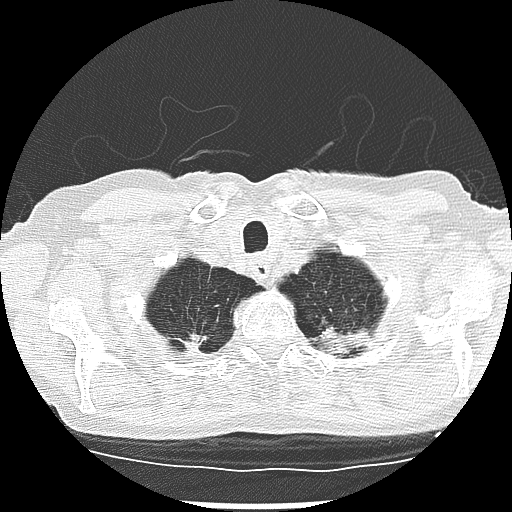
Low-dose screening chest CT, one axial slice. Slice 247 of 265 in the series (ordered by position). Reconstruction kernel LUNG. Lung window (W 1500 / L -600 HU). 2.5 mm slice thickness. 512 × 512 image matrix, field of view 300 × 300 mm.
Structures marked on this image (outlined manually by an expert reader):
- lesion 2 (tumor, upper lobe of right lung): bounding box (x1, y1, x2, y2) in pixels: (186, 336, 203, 349)